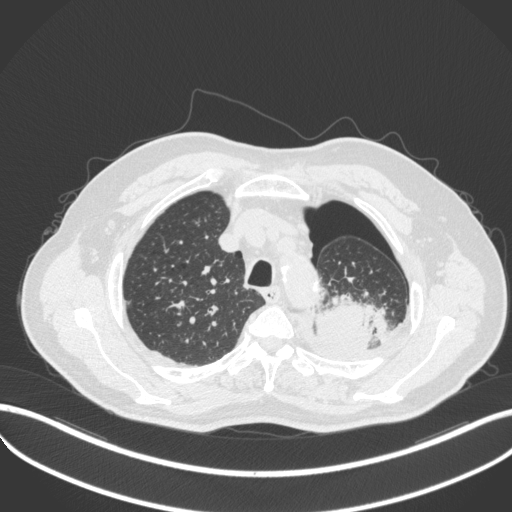
Chest CT, one axial slice; position 403 of 466 along the scan axis; reconstruction kernel B31f; lung window (W 1500 / L -600 HU); 1 mm slice thickness; 512 × 512 image matrix, field of view 400 × 400 mm. Patient: male, 76 years. Case-level facts recorded for this patient, not image findings: clinical TNM (as recorded): T3 N0 M1b.
Annotated regions visible in this slice (bounding box drawn by a radiologist):
- lung tumour (recorded histology: adenocarcinoma): bounding box <310,291,384,355> (left, top, right, bottom; pixels)